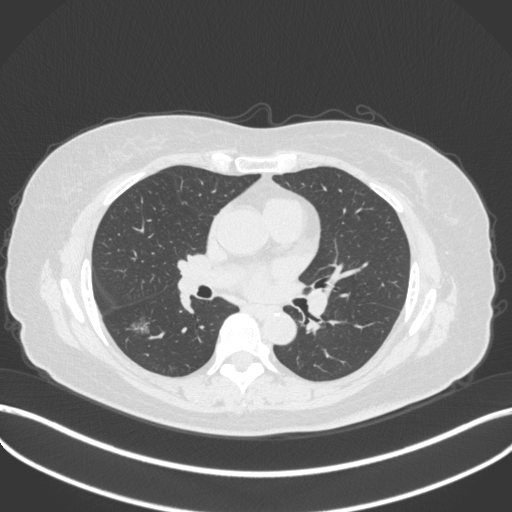
Chest CT, one axial slice; position 169 of 322 along the scan axis; reconstruction kernel B31f; lung window (W 1500 / L -600 HU); 1 mm slice thickness; 512 × 512 image matrix, field of view 400 × 400 mm. Female patient, age 64 years. Case-level facts recorded for this patient, not image findings: clinical TNM (as recorded): T1c N0 M0.
Structures marked on this image (rectangle marked by the reading radiologist):
- lung tumour (recorded histology: adenocarcinoma): bounding box [x1, y1, x2, y2] px = [126, 314, 155, 343]